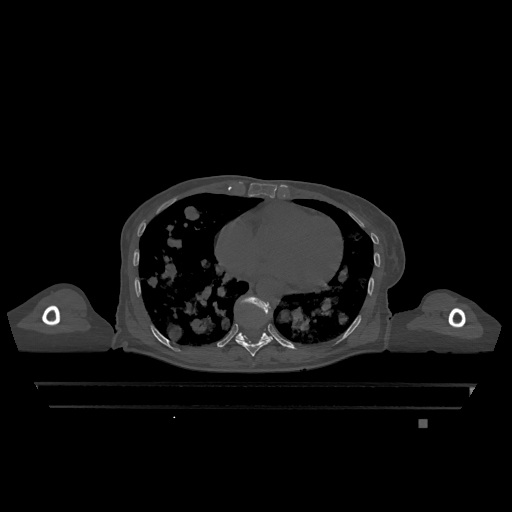
CT including the spine, one axial slice; position 674 of 1317 along the scan axis; bone window (W 1800 / L 400 HU); 0.5 mm slice thickness; 512 × 512 image matrix, field of view 500 × 500 mm. Patient: female, 74 years. From the clinical record (not read from this slice): primary cancer: lung; vertebrae with lytic lesions (as recorded): T1, T4, T5, T6, L4, L5.
Outlined on this slice (semi-automatically segmented with operator editing):
- T10 vertebra: bounding box [x1, y1, x2, y2] px = [235, 297, 273, 341]
- T9 vertebra: [236, 307, 272, 357]